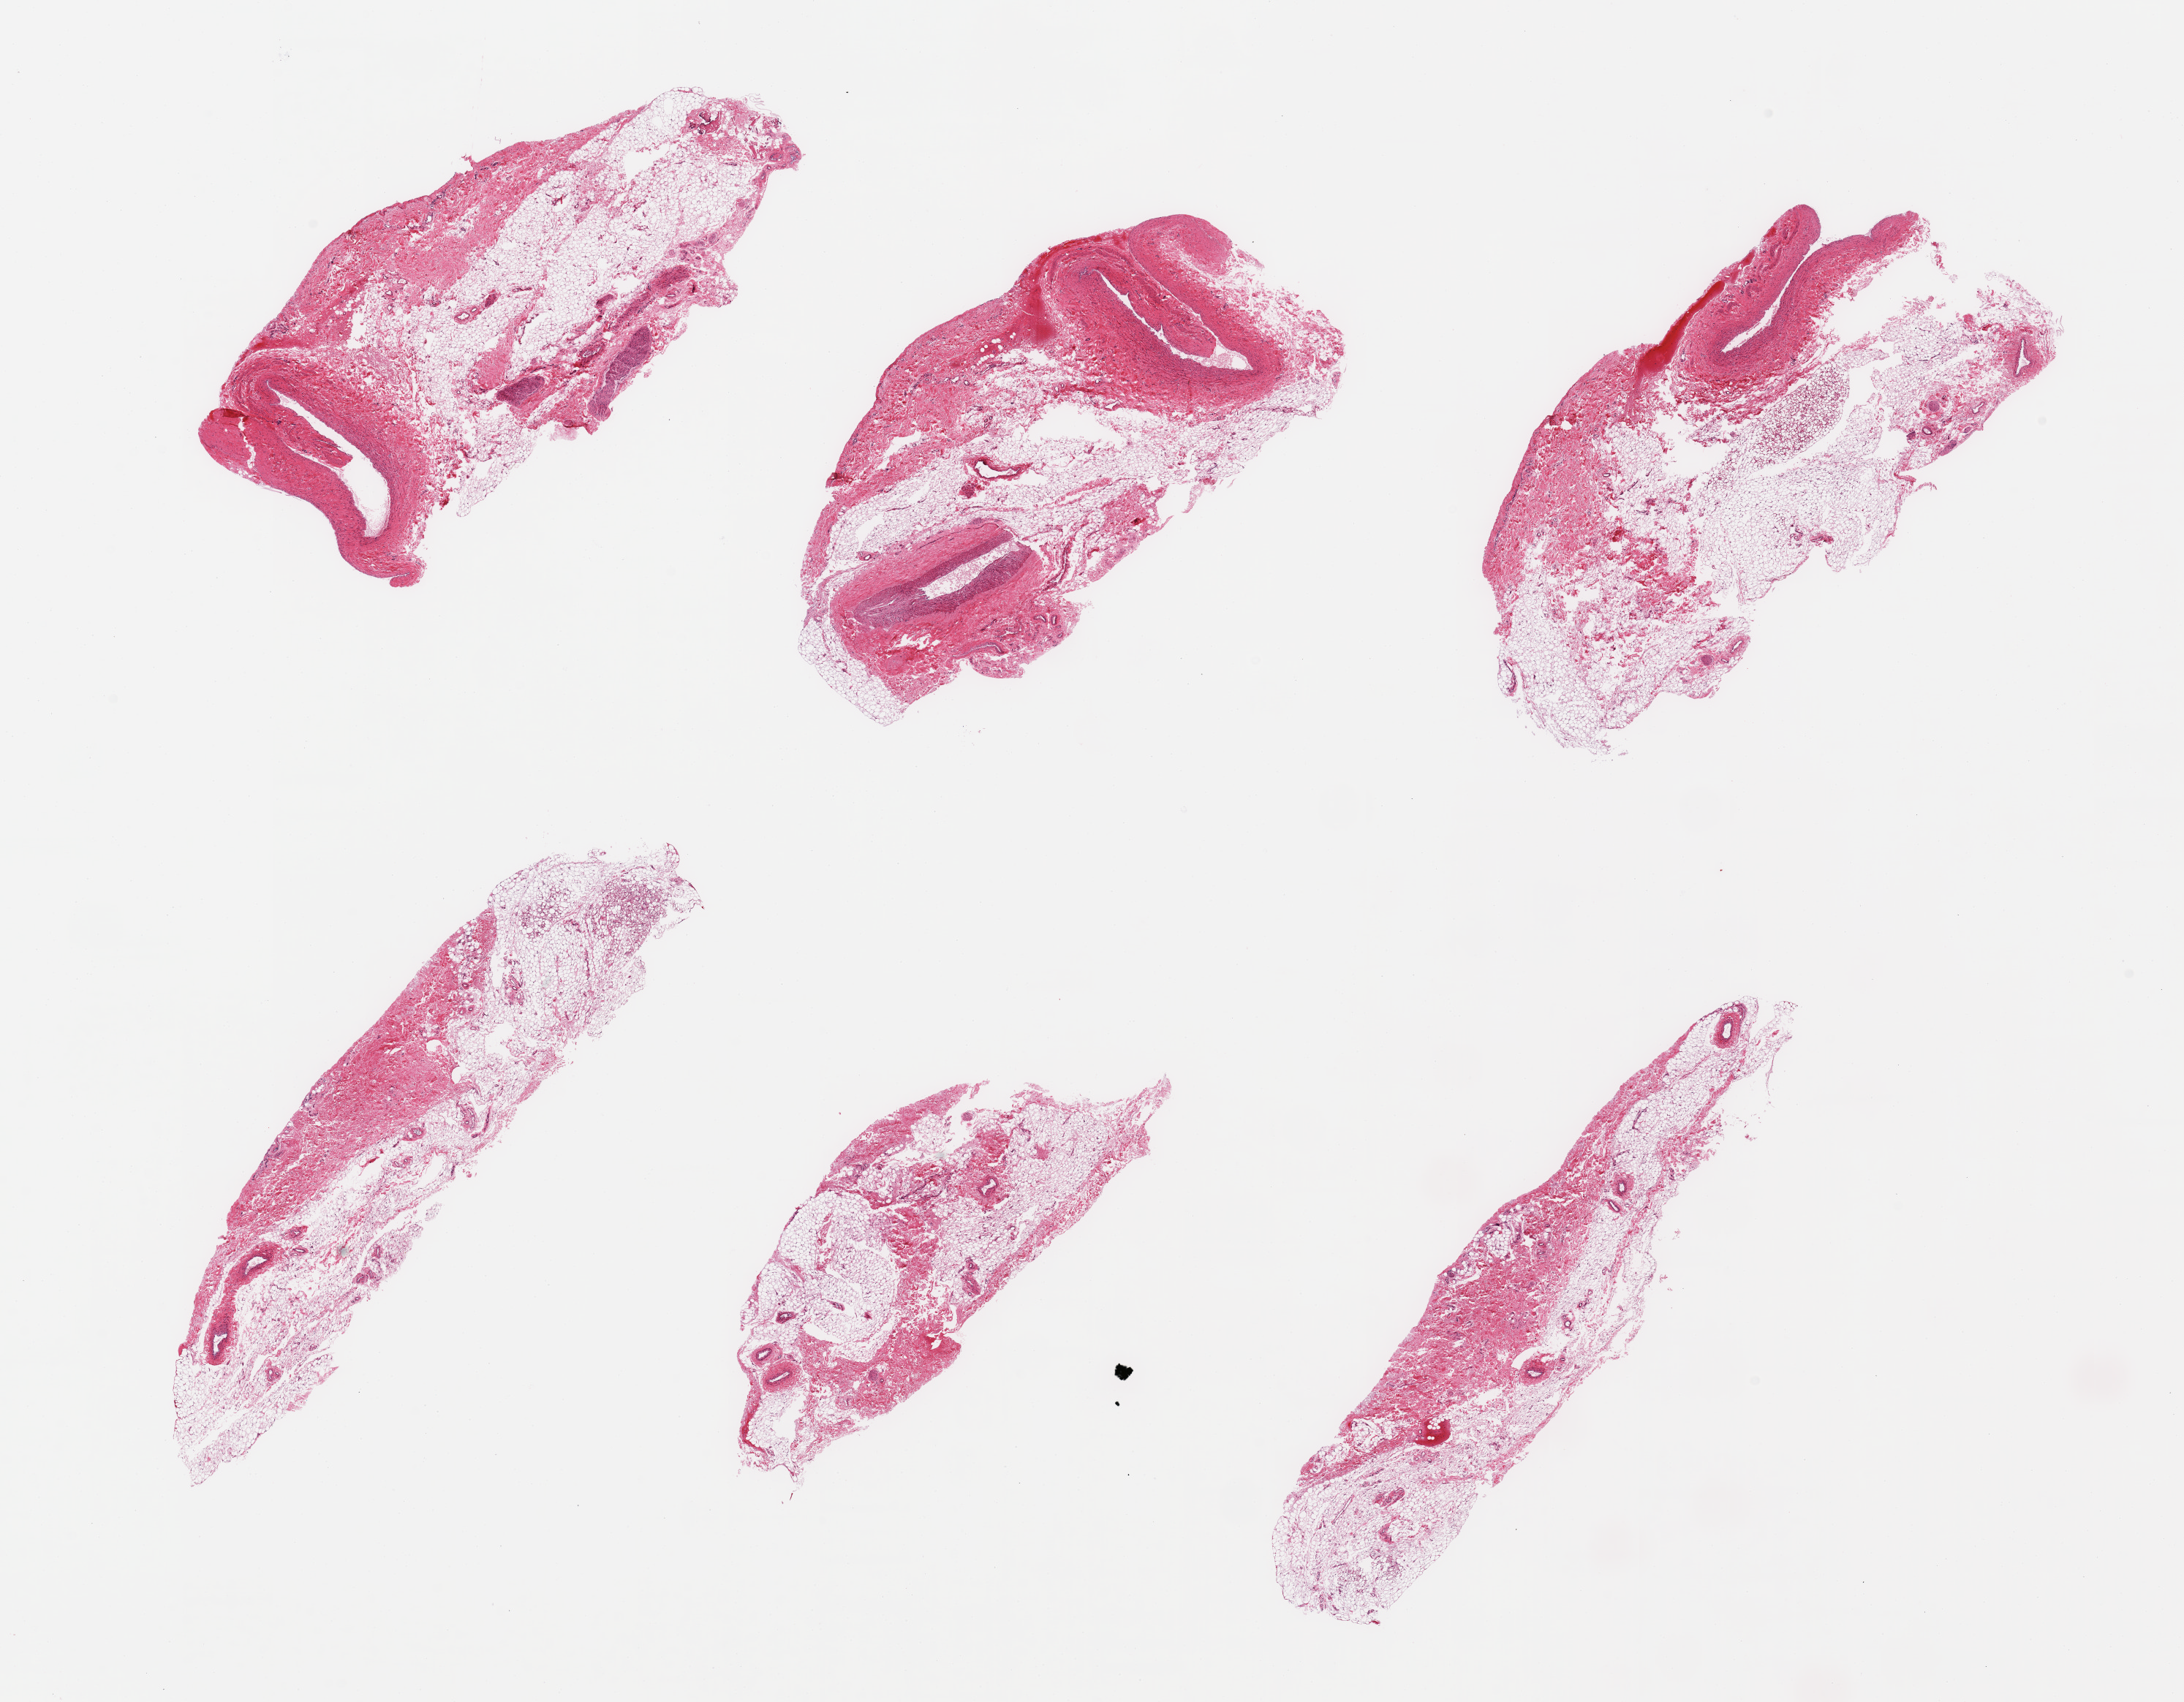
Whole-slide image, H&E stain, brightfield — a low-resolution overview of the entire scanned area, about 23.6 x 18.4 mm (from a 20x scan). PAXgene-fixed, paraffin-embedded tissue. Target tissue: esophageal mucous membrane. Donor tissue sample. Female donor.
Pathologist's review note for this sample: 6 pieces, fat and muscular artery, no esophageal mucosa or muscularis present.